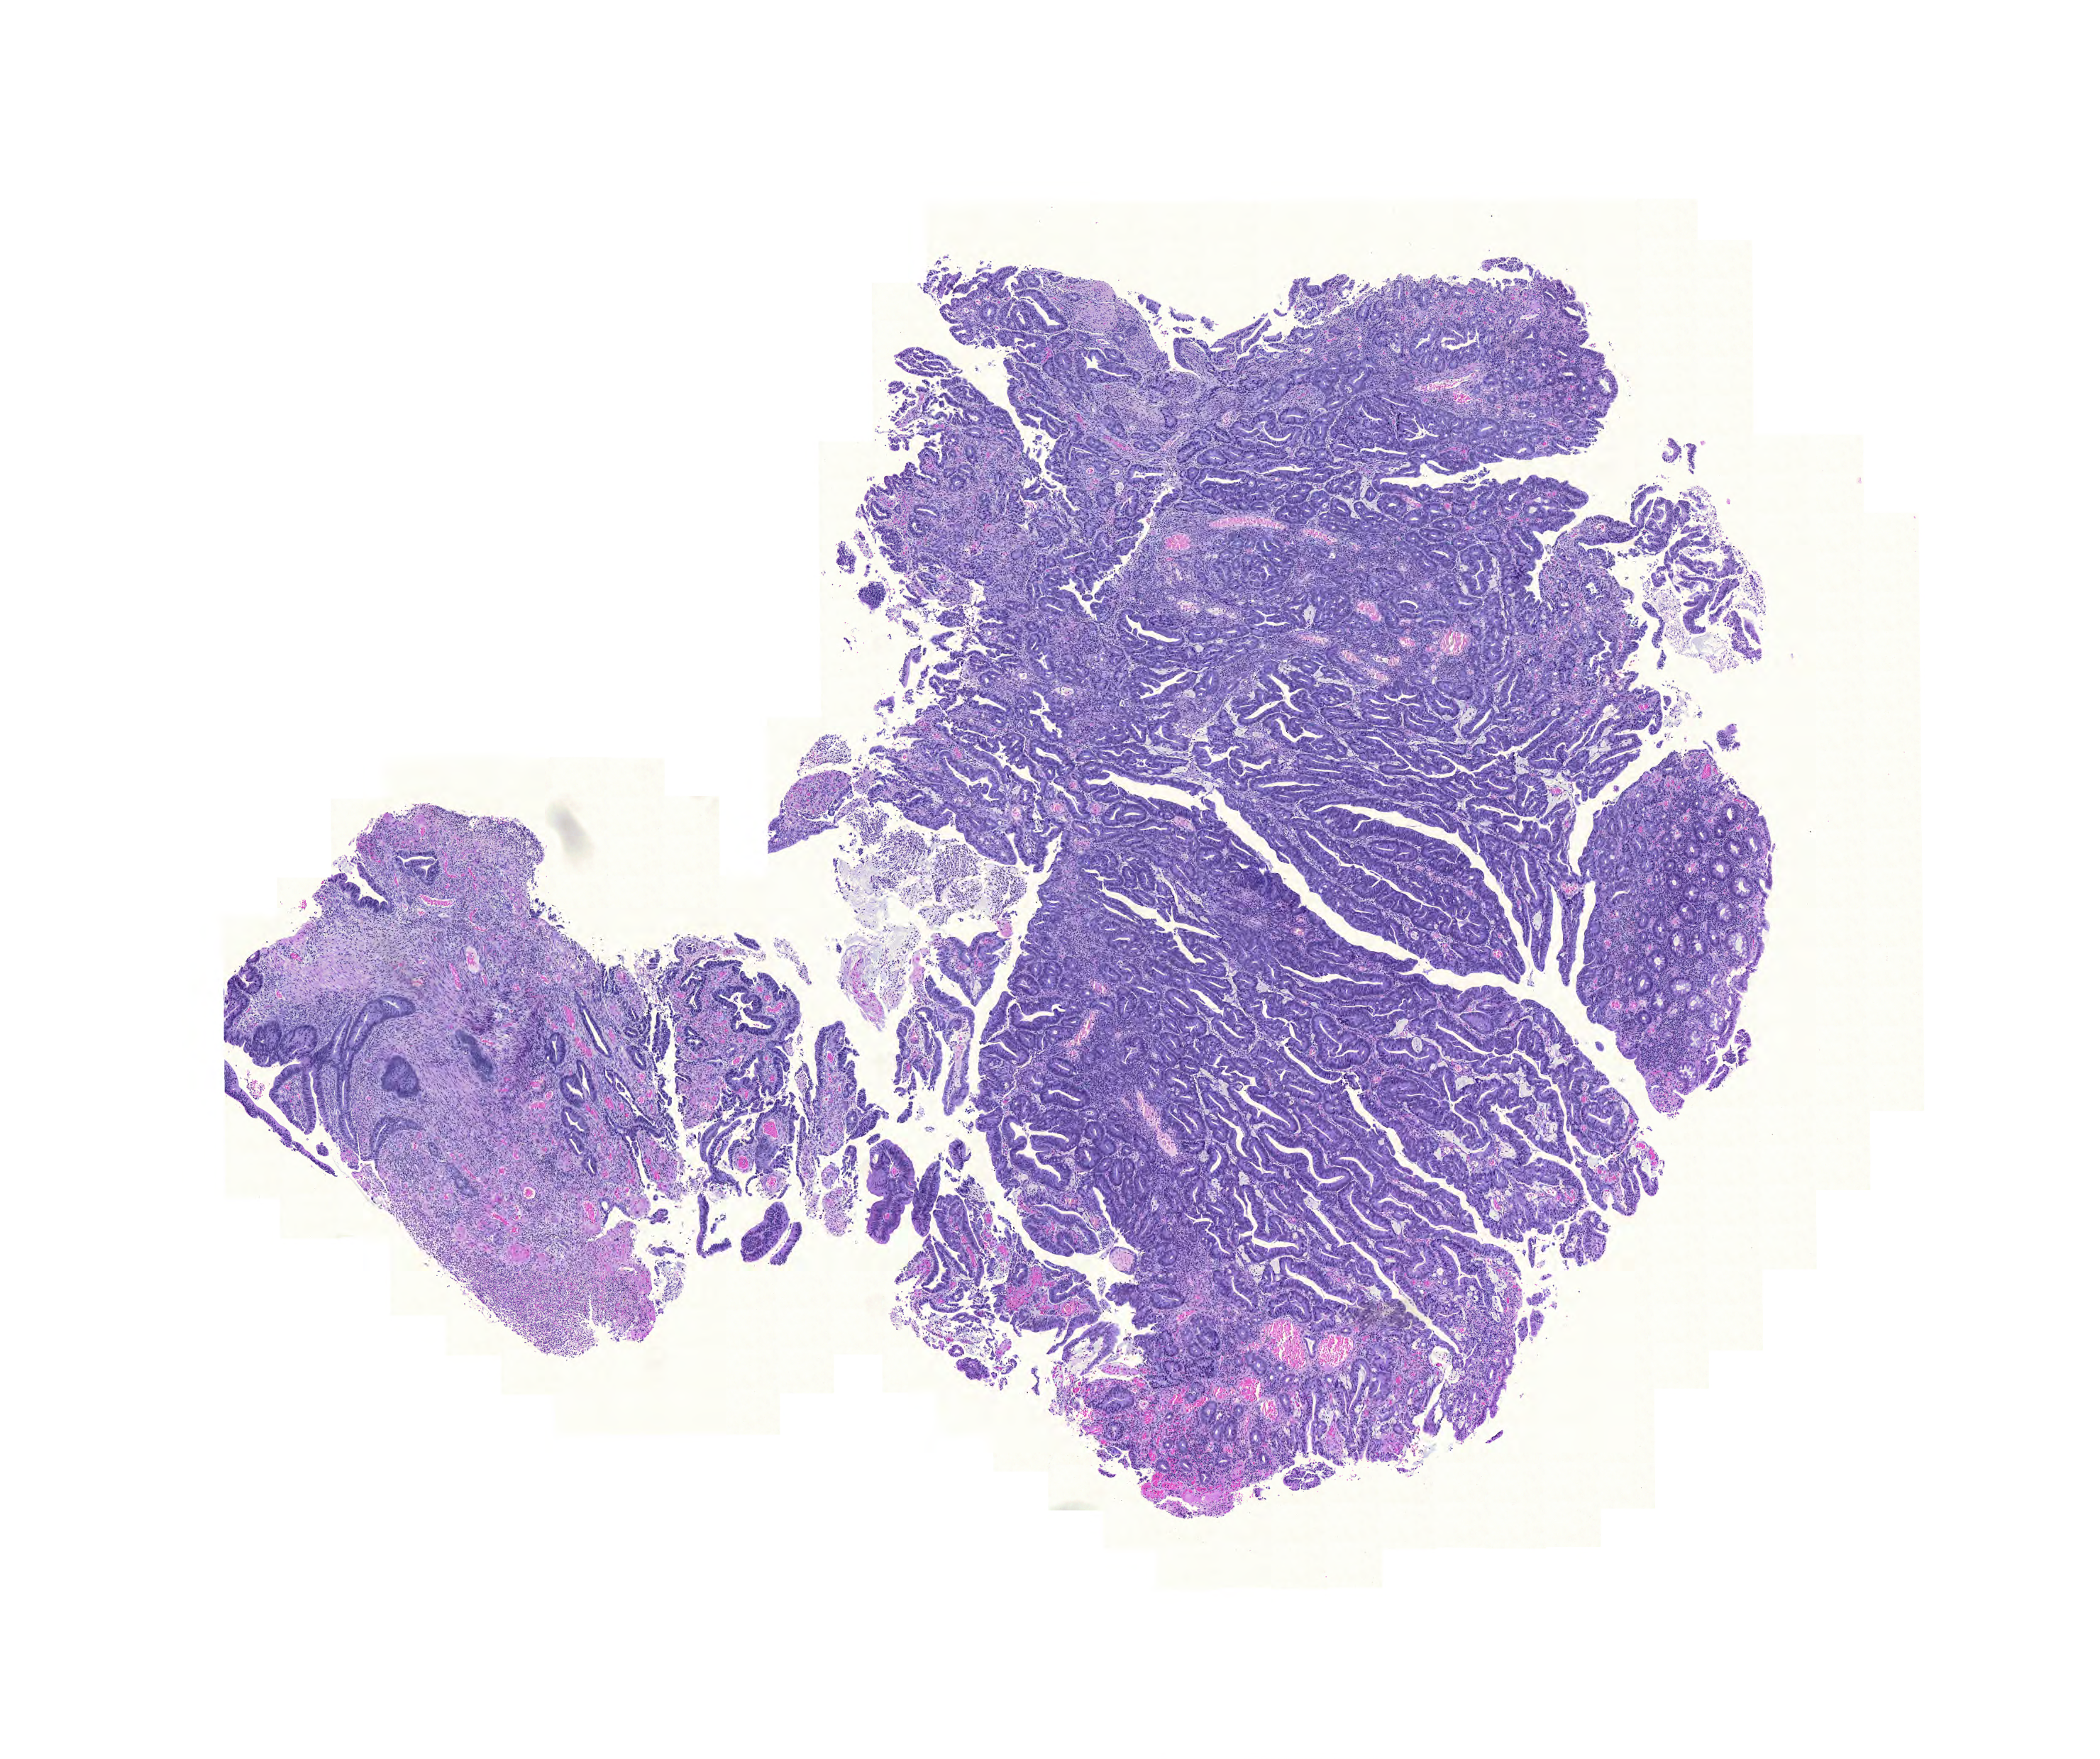
Whole-slide histology image, H&E-stained, shown as a low-resolution overview of the whole scanned area (about 11.0 x 9.2 mm); FFPE section; colon, primary tumour sample. Female, age 72 years at initial diagnosis.
Lymph nodes positive (case pathology): 5 of 25 examined. Pathologic diagnosis: Adenocarcinoma, NOS (sigmoid colon). AJCC pathologic stage: IIIC (6th edition).